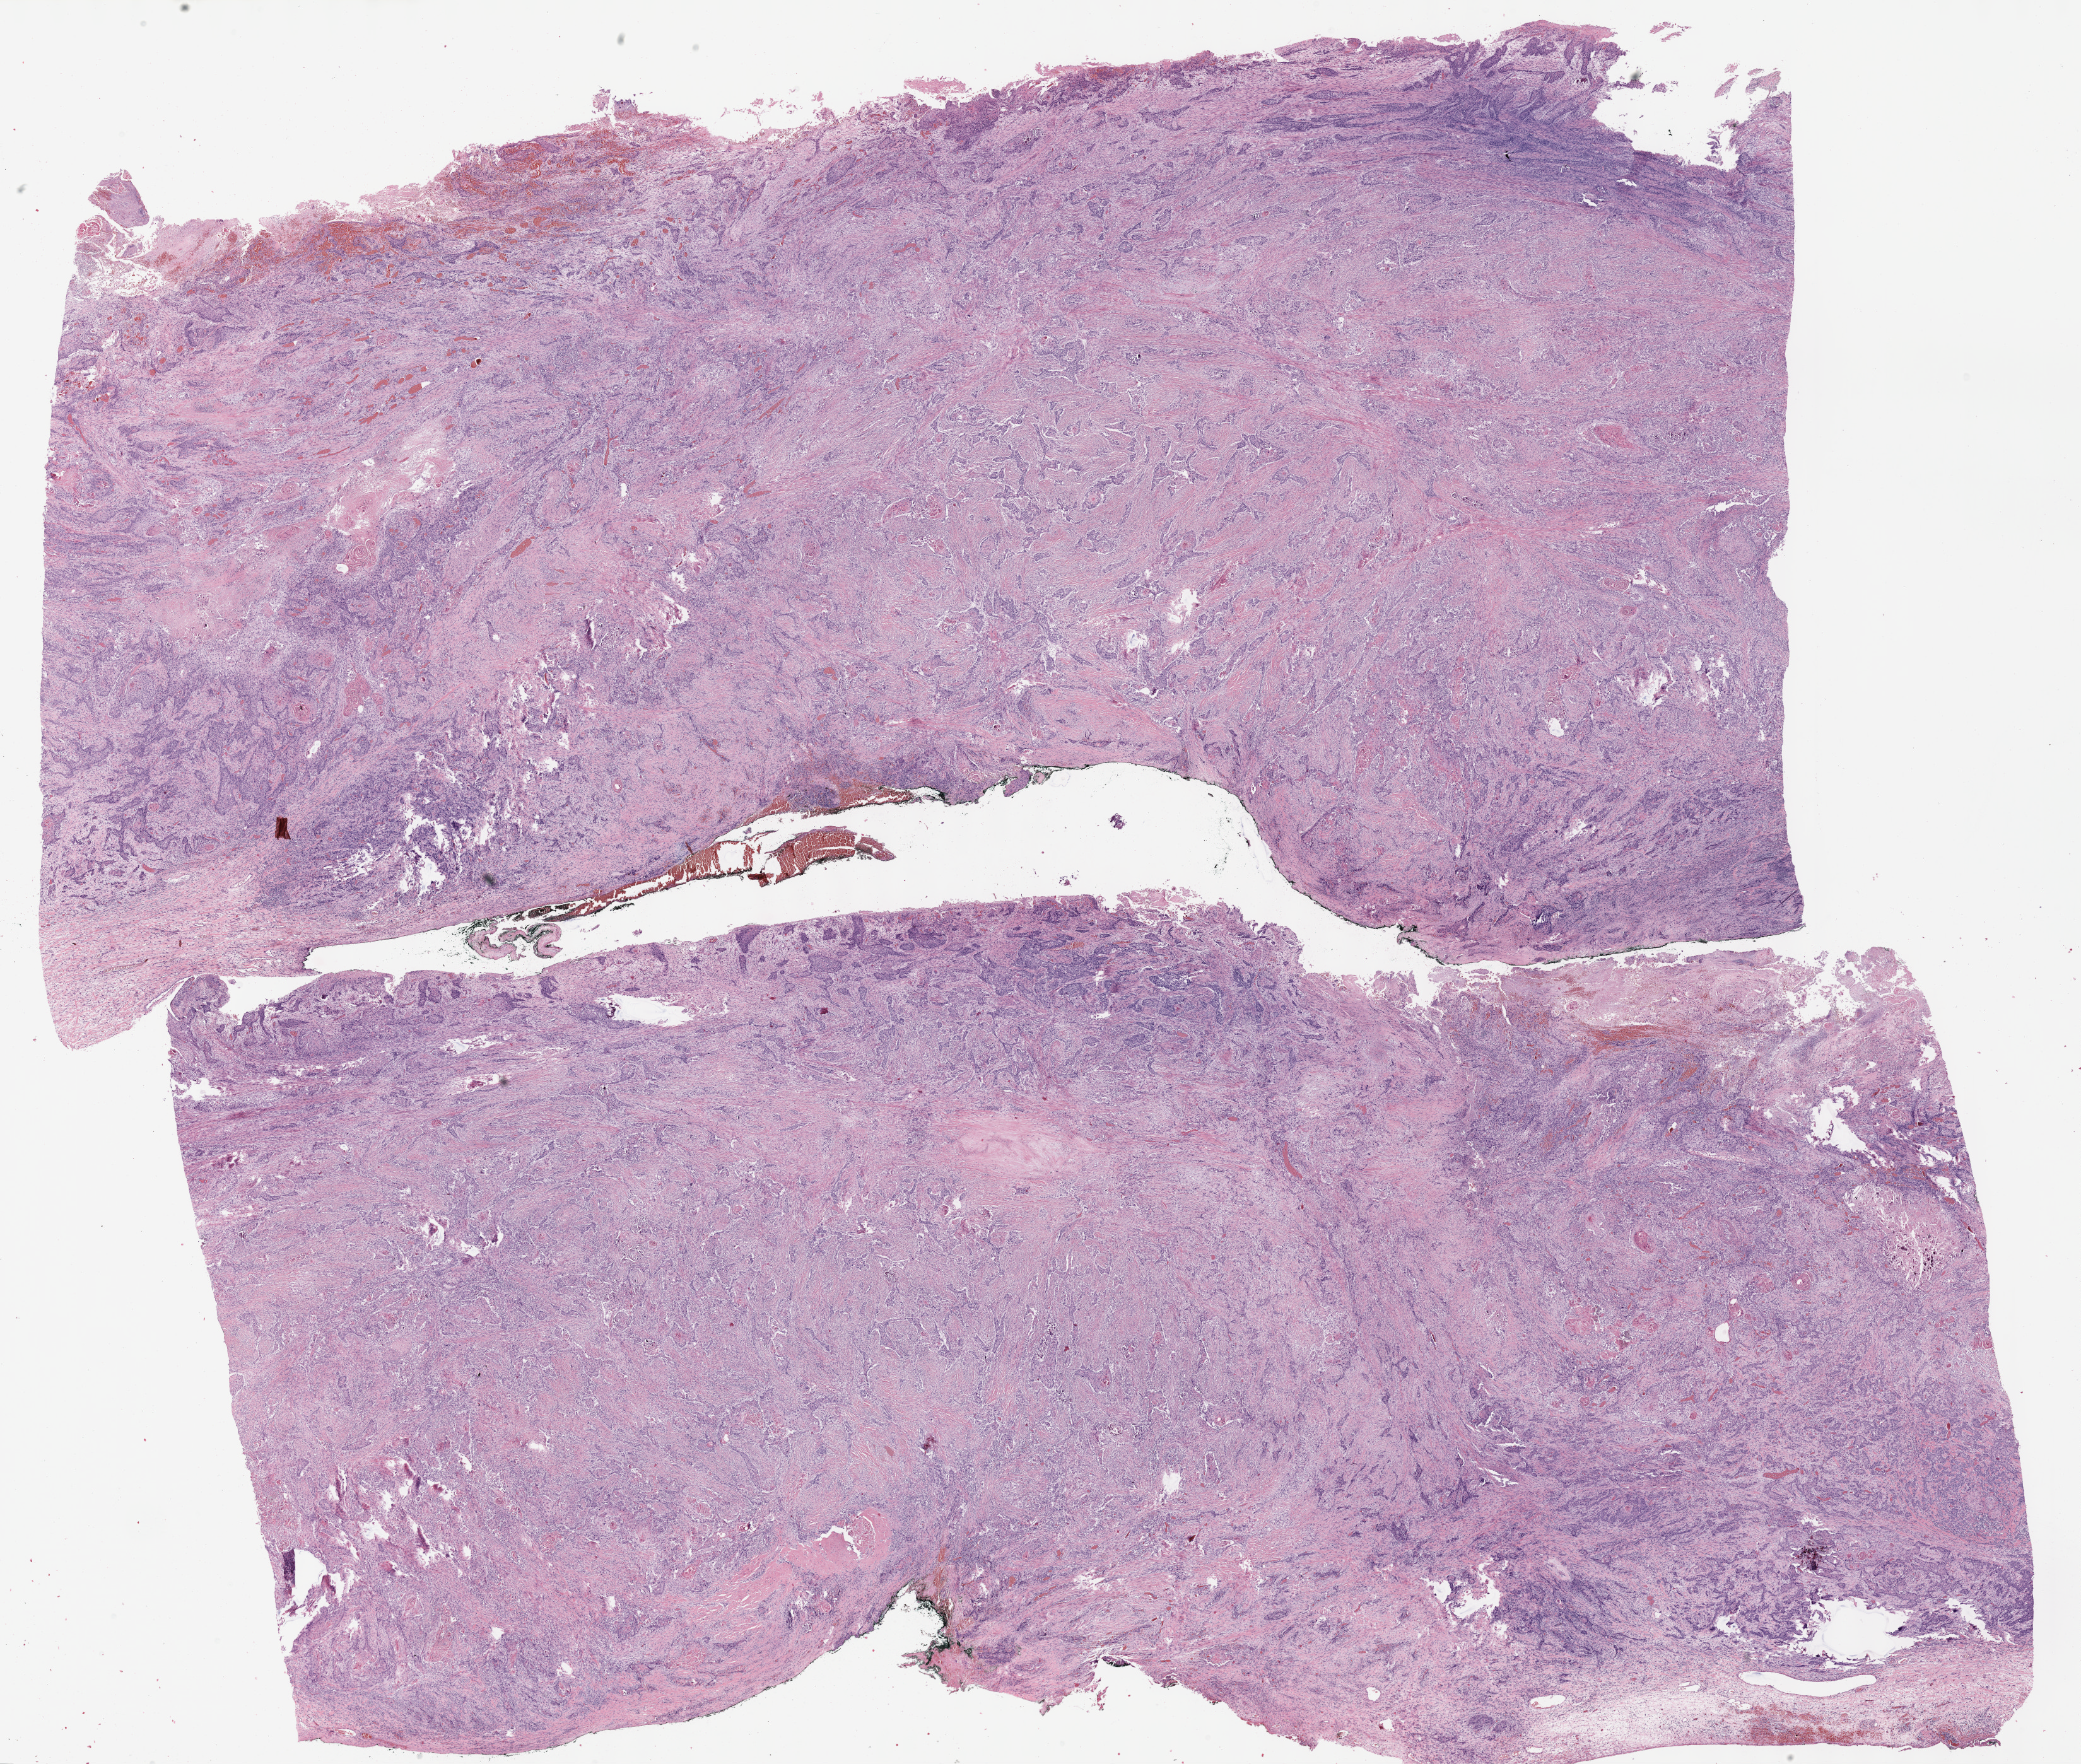
Hematoxylin and eosin (H&E) stained whole-slide image — shown as a low-resolution overview of the whole scanned area (about 26.7 x 22.6 mm, from a 40x scan); formalin-fixed paraffin-embedded (FFPE) diagnostic section; sample: primary tumour, esophagus. Male, age 70 years at initial diagnosis. Histologic grade: G1 (well differentiated).
Lymph nodes positive (case pathology): 0 of 15 examined. AJCC pathologic stage: III. Pathologic diagnosis: Squamous cell carcinoma, NOS (middle third of esophagus).